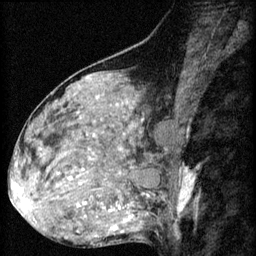
Breast MRI (dynamic contrast-enhanced), one sagittal slice; slice 33 of 60 in the series (ordered by position); 3 images stored at this slice position (order not interpretable as contrast timing); 1.5 T; TE 4.2 ms, TR 8.2 ms; 2 mm slice thickness; 256 × 256 image matrix. Patient: female, 48 years.
Outlined on this slice (semi-automatically segmented with operator editing):
- analysis volume of interest (the breast-tissue region the enhancement analysis was run in; not a lesion): box from (x=48, y=160) to (x=125, y=217) px
- tumour enhancement mask (voxels above the 70 % enhancement threshold inside the analysis volume of interest): (x=57, y=174)–(x=120, y=209)